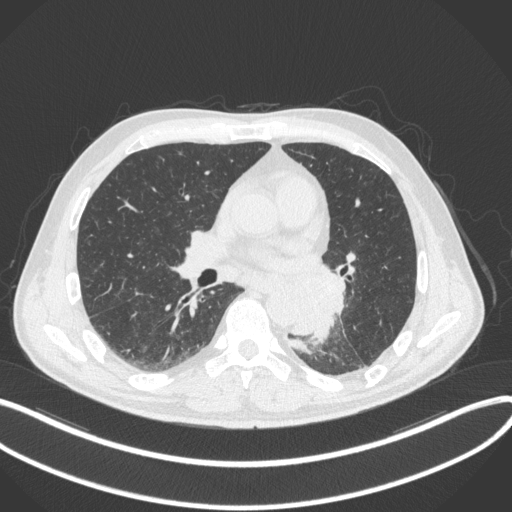
Chest CT, one axial slice. Lung window (W 1500 / L -600 HU). 1 mm slice thickness. 512 × 512 image matrix, field of view 400 × 400 mm. Patient: male, 59 years. From the clinical record (not read from this slice): clinical TNM (as recorded): T2a N2 M0.
Outlined on this slice (bounding box drawn by a radiologist):
- lung tumour (recorded histology: squamous cell carcinoma): bounding box [x1, y1, x2, y2] px = [290, 262, 350, 346]